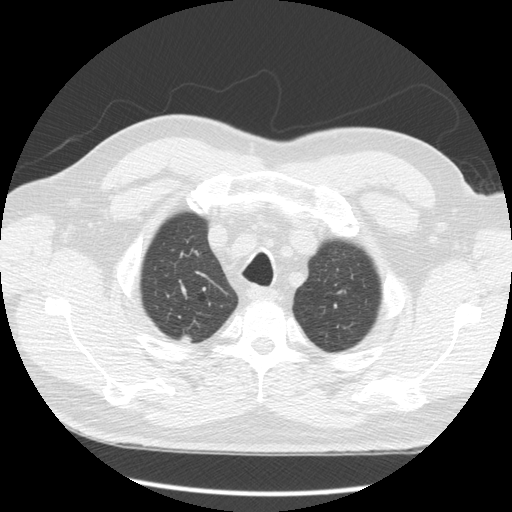
Low-dose screening chest CT, axial slice, first (baseline) screen, lung window (W 1500 / L -600 HU). Male, age 65 years at enrolment. Former smoker at enrolment.
Expert-annotated lung lesion, bounding box <165,323,204,357> (left, top, right, bottom; pixels). Reader record for this screening exam (exam-level; its link to the box is not recorded): non-calcified nodule or mass ≥4 mm, right upper lobe, 10 × 9 mm, spiculated (stellate) margins, soft tissue attenuation. Later outcome: lung cancer diagnosed 103 days after this screen — squamous cell carcinoma, NOS, right upper lobe, poorly differentiated (G3), stage IA (AJCC 6th edition), 5 mm at pathology.